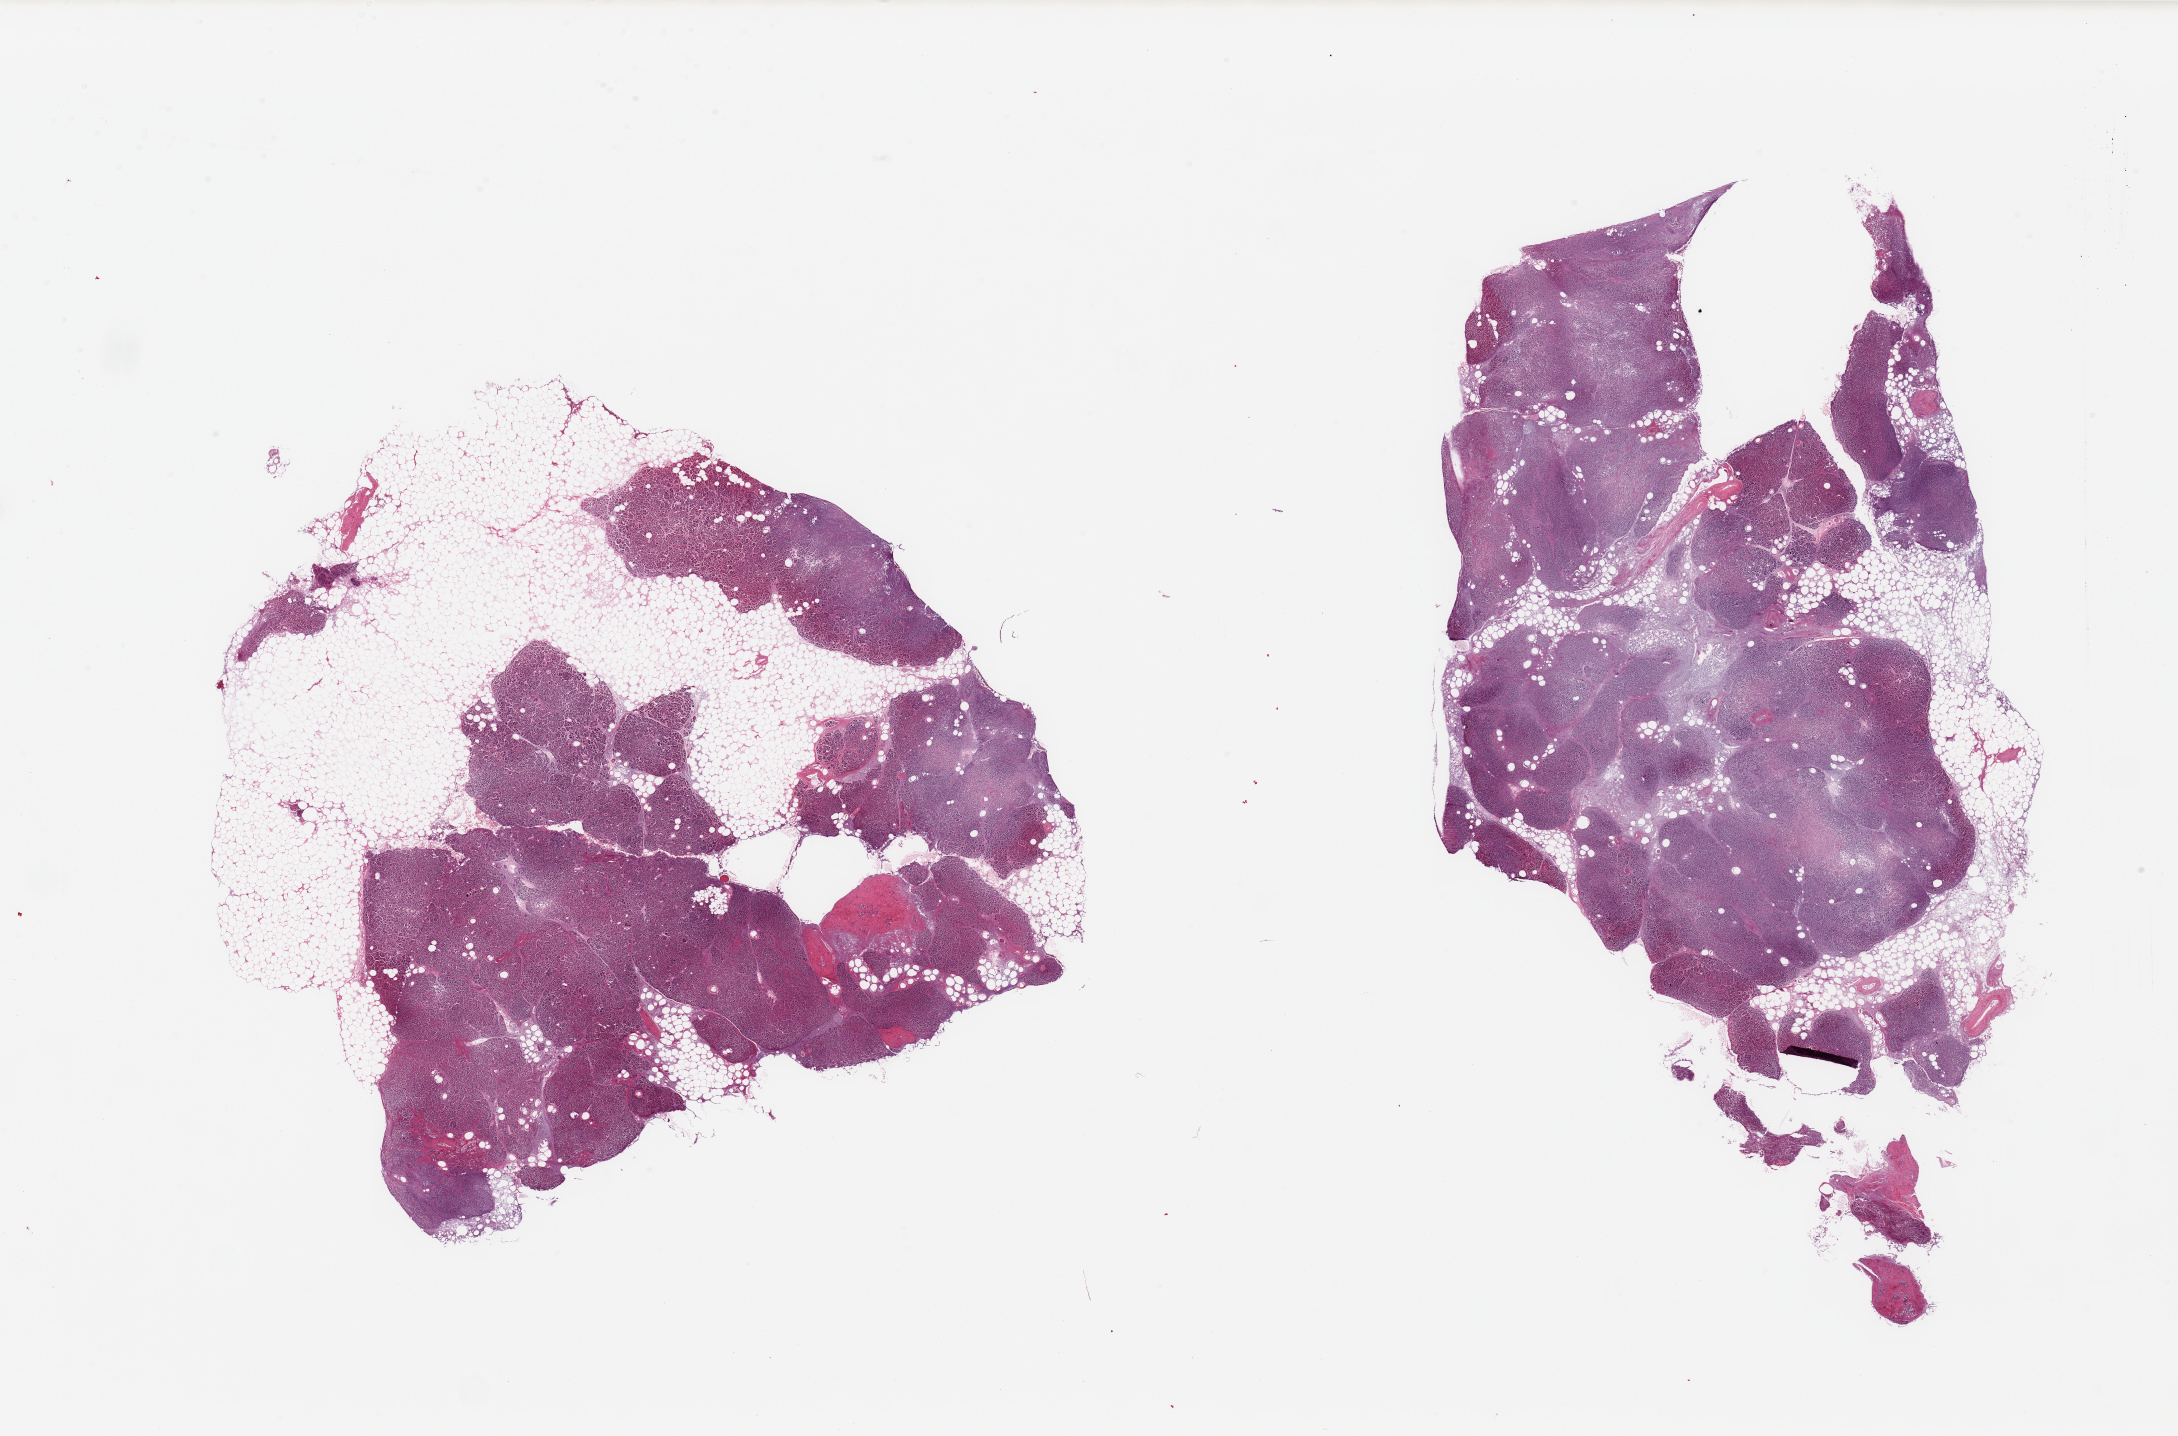
Whole-slide image, H&E stain, brightfield, low-resolution overview of the scanned area, about 34.5 x 22.7 mm. PAXgene-fixed, paraffin-embedded tissue. Sampled site (target tissue): pancreas. Tissue donor sample.
Reviewer comment on this tissue sample: 2 pieces; moderate to severe autolysis of parenchyma and associated septal fat; 50% and 20% external fat; rare Langerhans islets.